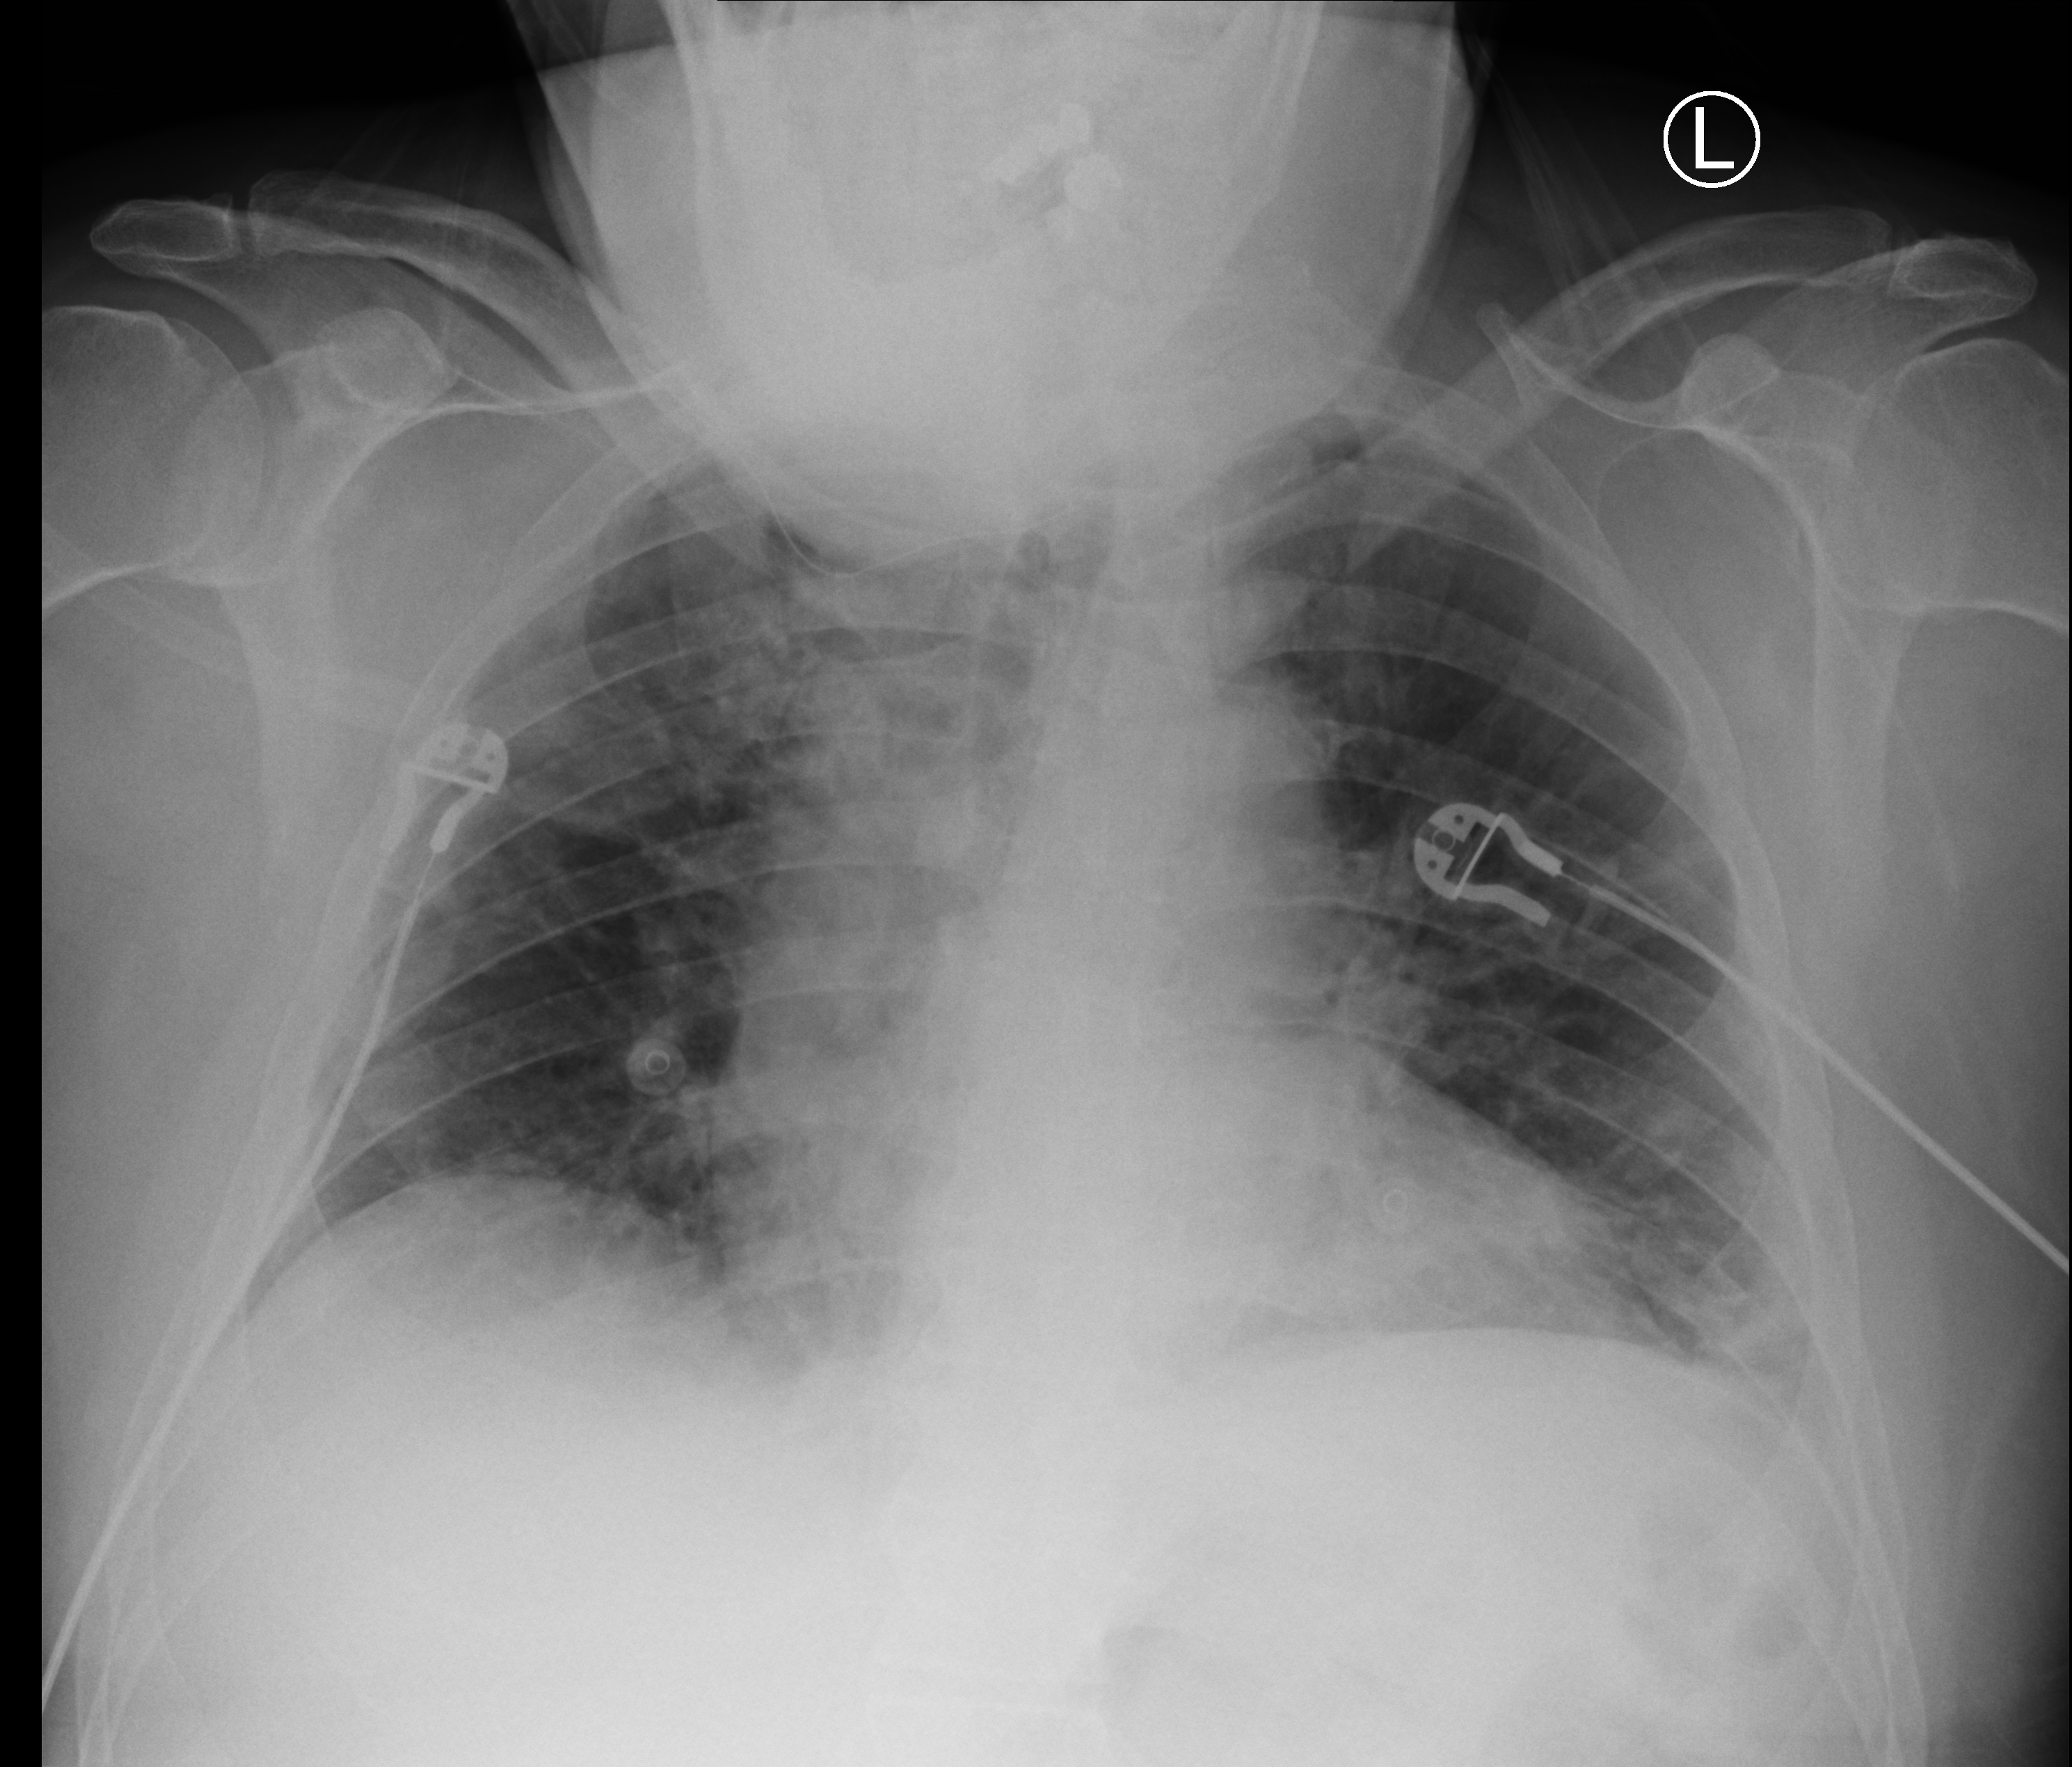
Bedside chest radiograph (computed radiography); anteroposterior (AP) projection. Male patient hospitalised with COVID-19, age 60–74 years.
Hospital-stay facts (about this admission, not read from this image; timing relative to this image not recorded):
- mechanically ventilated during this hospital stay: no
- other chronic lung disease (admission record): no
- admitted to intensive care during this hospital stay: no